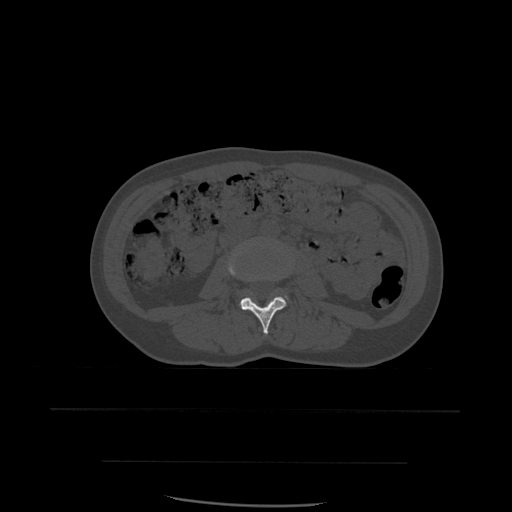
CT including the spine, one axial slice. Slice 189 of 574 in the series (ordered by position). Bone window (W 1800 / L 400 HU). 512 × 512 image matrix, field of view 392 × 392 mm. Patient age 48 years. From the clinical record (not read from this slice): primary cancer: lung; vertebrae with lytic lesions (as recorded): T11.
Structures marked on this image (semi-automatic segmentation, software-assisted and operator-edited):
- L3 vertebra: bounding box (x1, y1, x2, y2) in pixels: (228, 247, 287, 335)